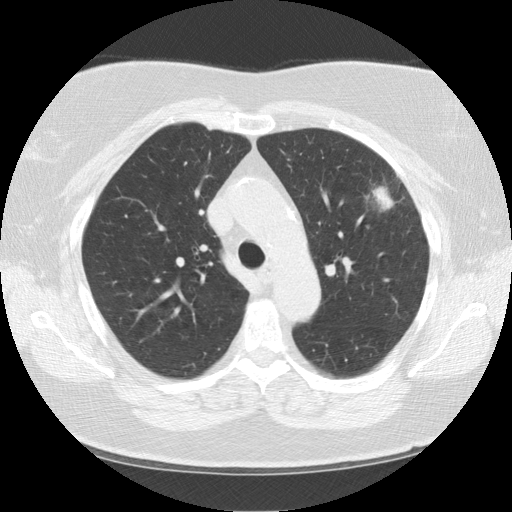
Low-dose screening chest CT, axial slice; baseline annual screen; lung window (W 1500 / L -600 HU); 2.5 mm slice thickness; standard (soft-tissue) reconstruction kernel (STANDARD); 120 kVp; slice 38 of 130 in the series. Female, age 67 years at enrolment. Former smoker at enrolment.
- Expert-annotated lung lesion, bounding box <346,155,423,230> (left, top, right, bottom; pixels).
- The exam's reader record, not a measurement of the box and not confirmed to be the same lesion: non-calcified nodule or mass ≥4 mm, left upper lobe, 28 × 19 mm, soft tissue attenuation.
- Later outcome: lung cancer diagnosed 33 days after this screen — squamous cell carcinoma, NOS, left upper lobe, poorly differentiated (G3), stage IA (AJCC 6th edition), 25 mm at pathology.